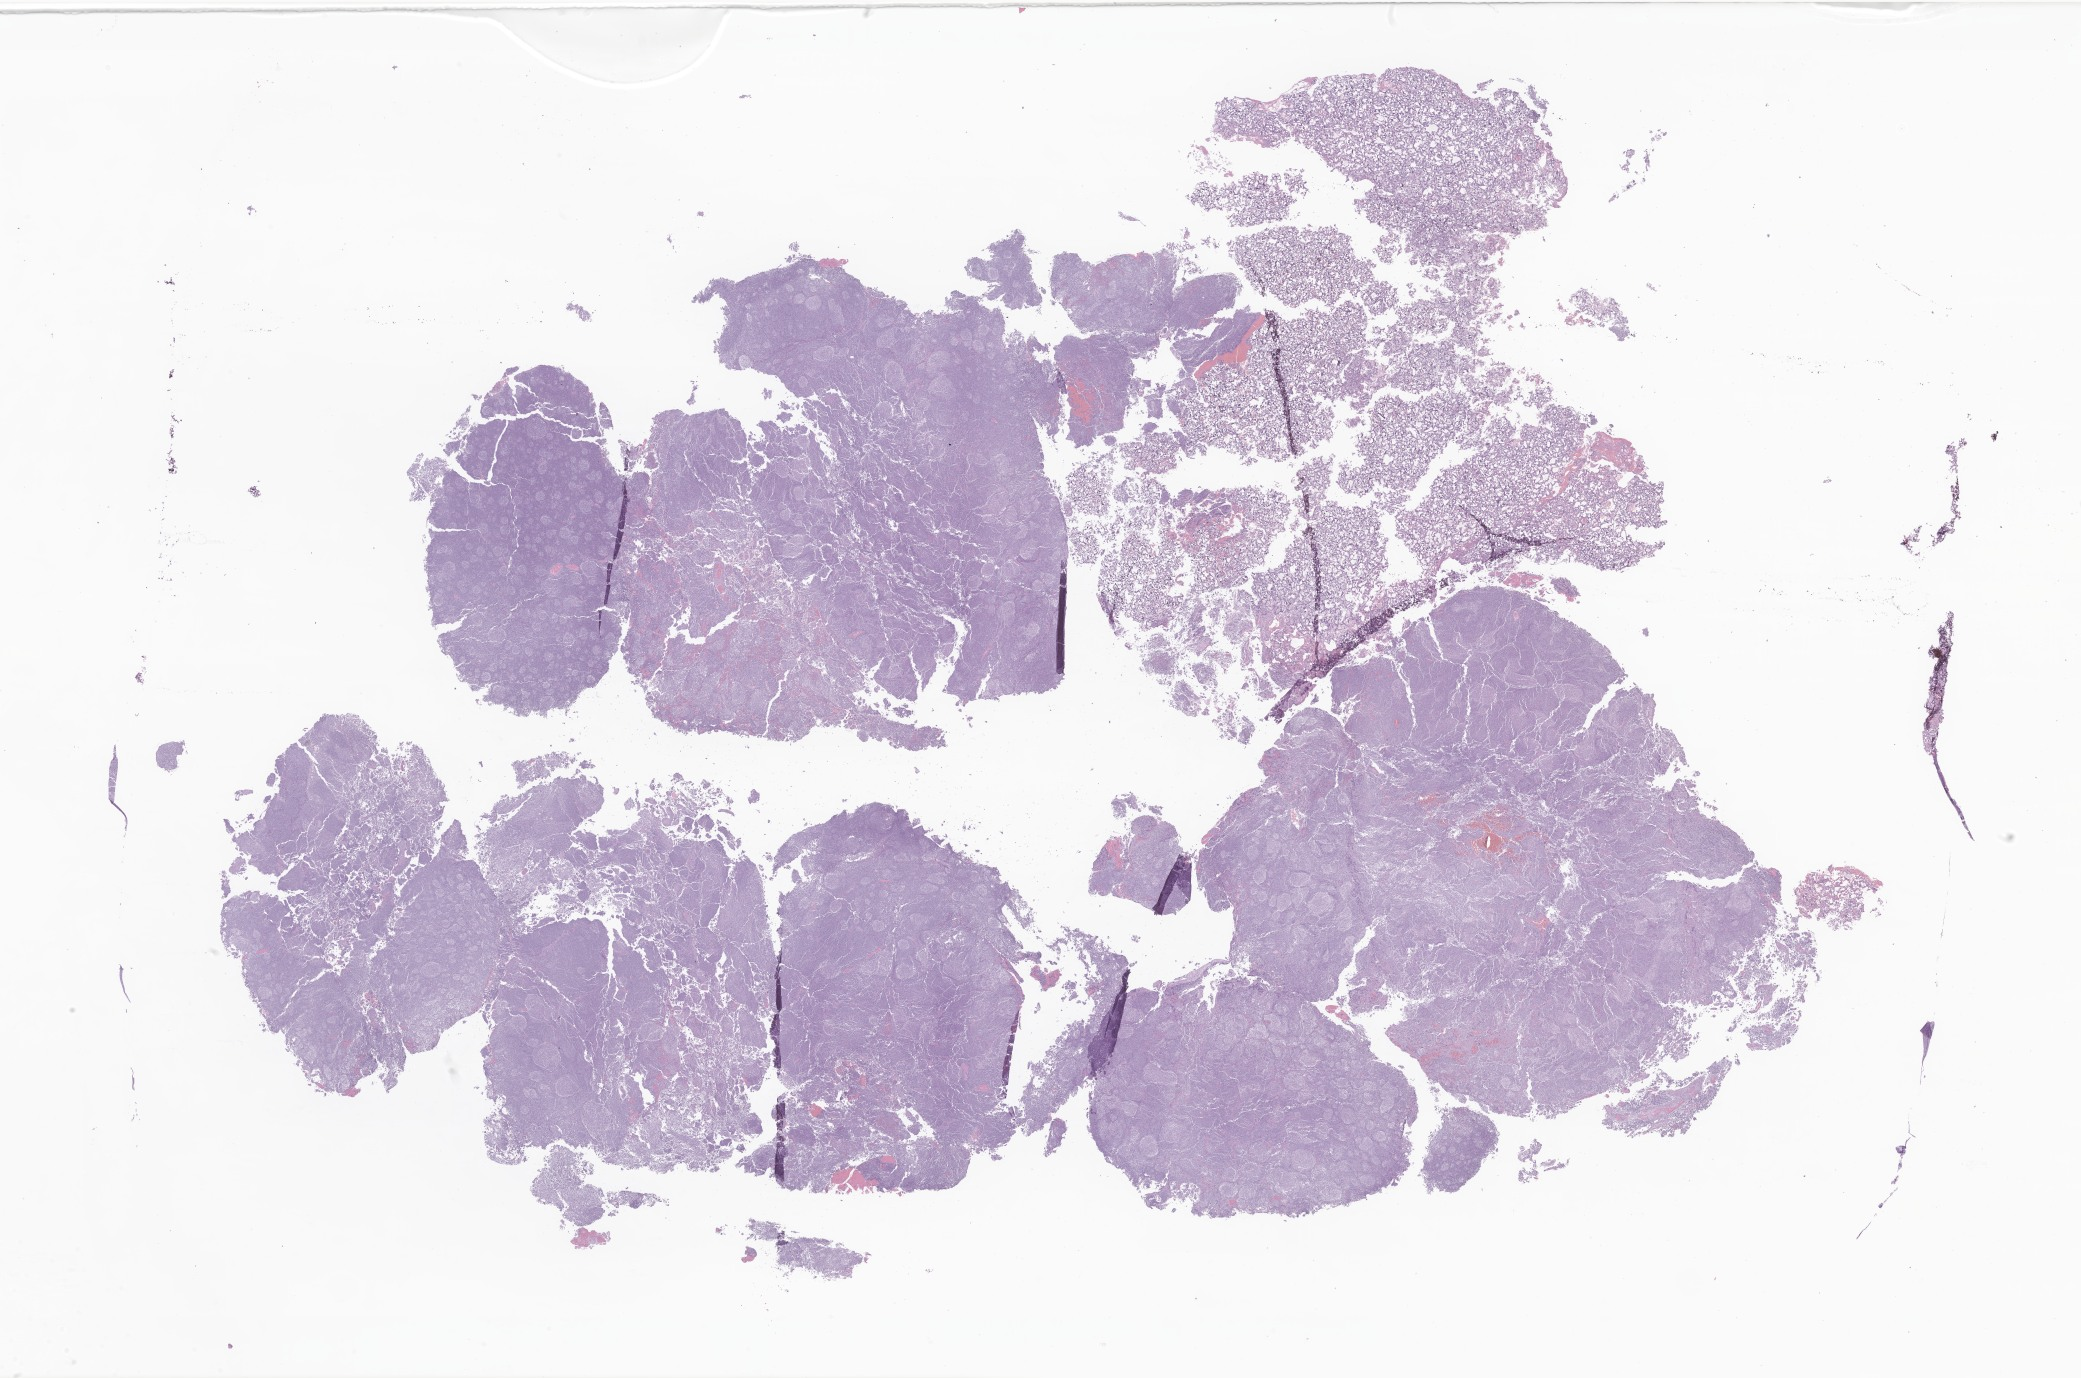
H&E whole-slide image of tumor tissue from the cerebellum — whole scanned area (about 35.1 x 23.2 mm) shown as a low-resolution overview, formalin-fixed paraffin-embedded section. Patient: male, age 218 months (18 years 2 months).
Recorded diagnosis: Medulloblastoma, NOS.